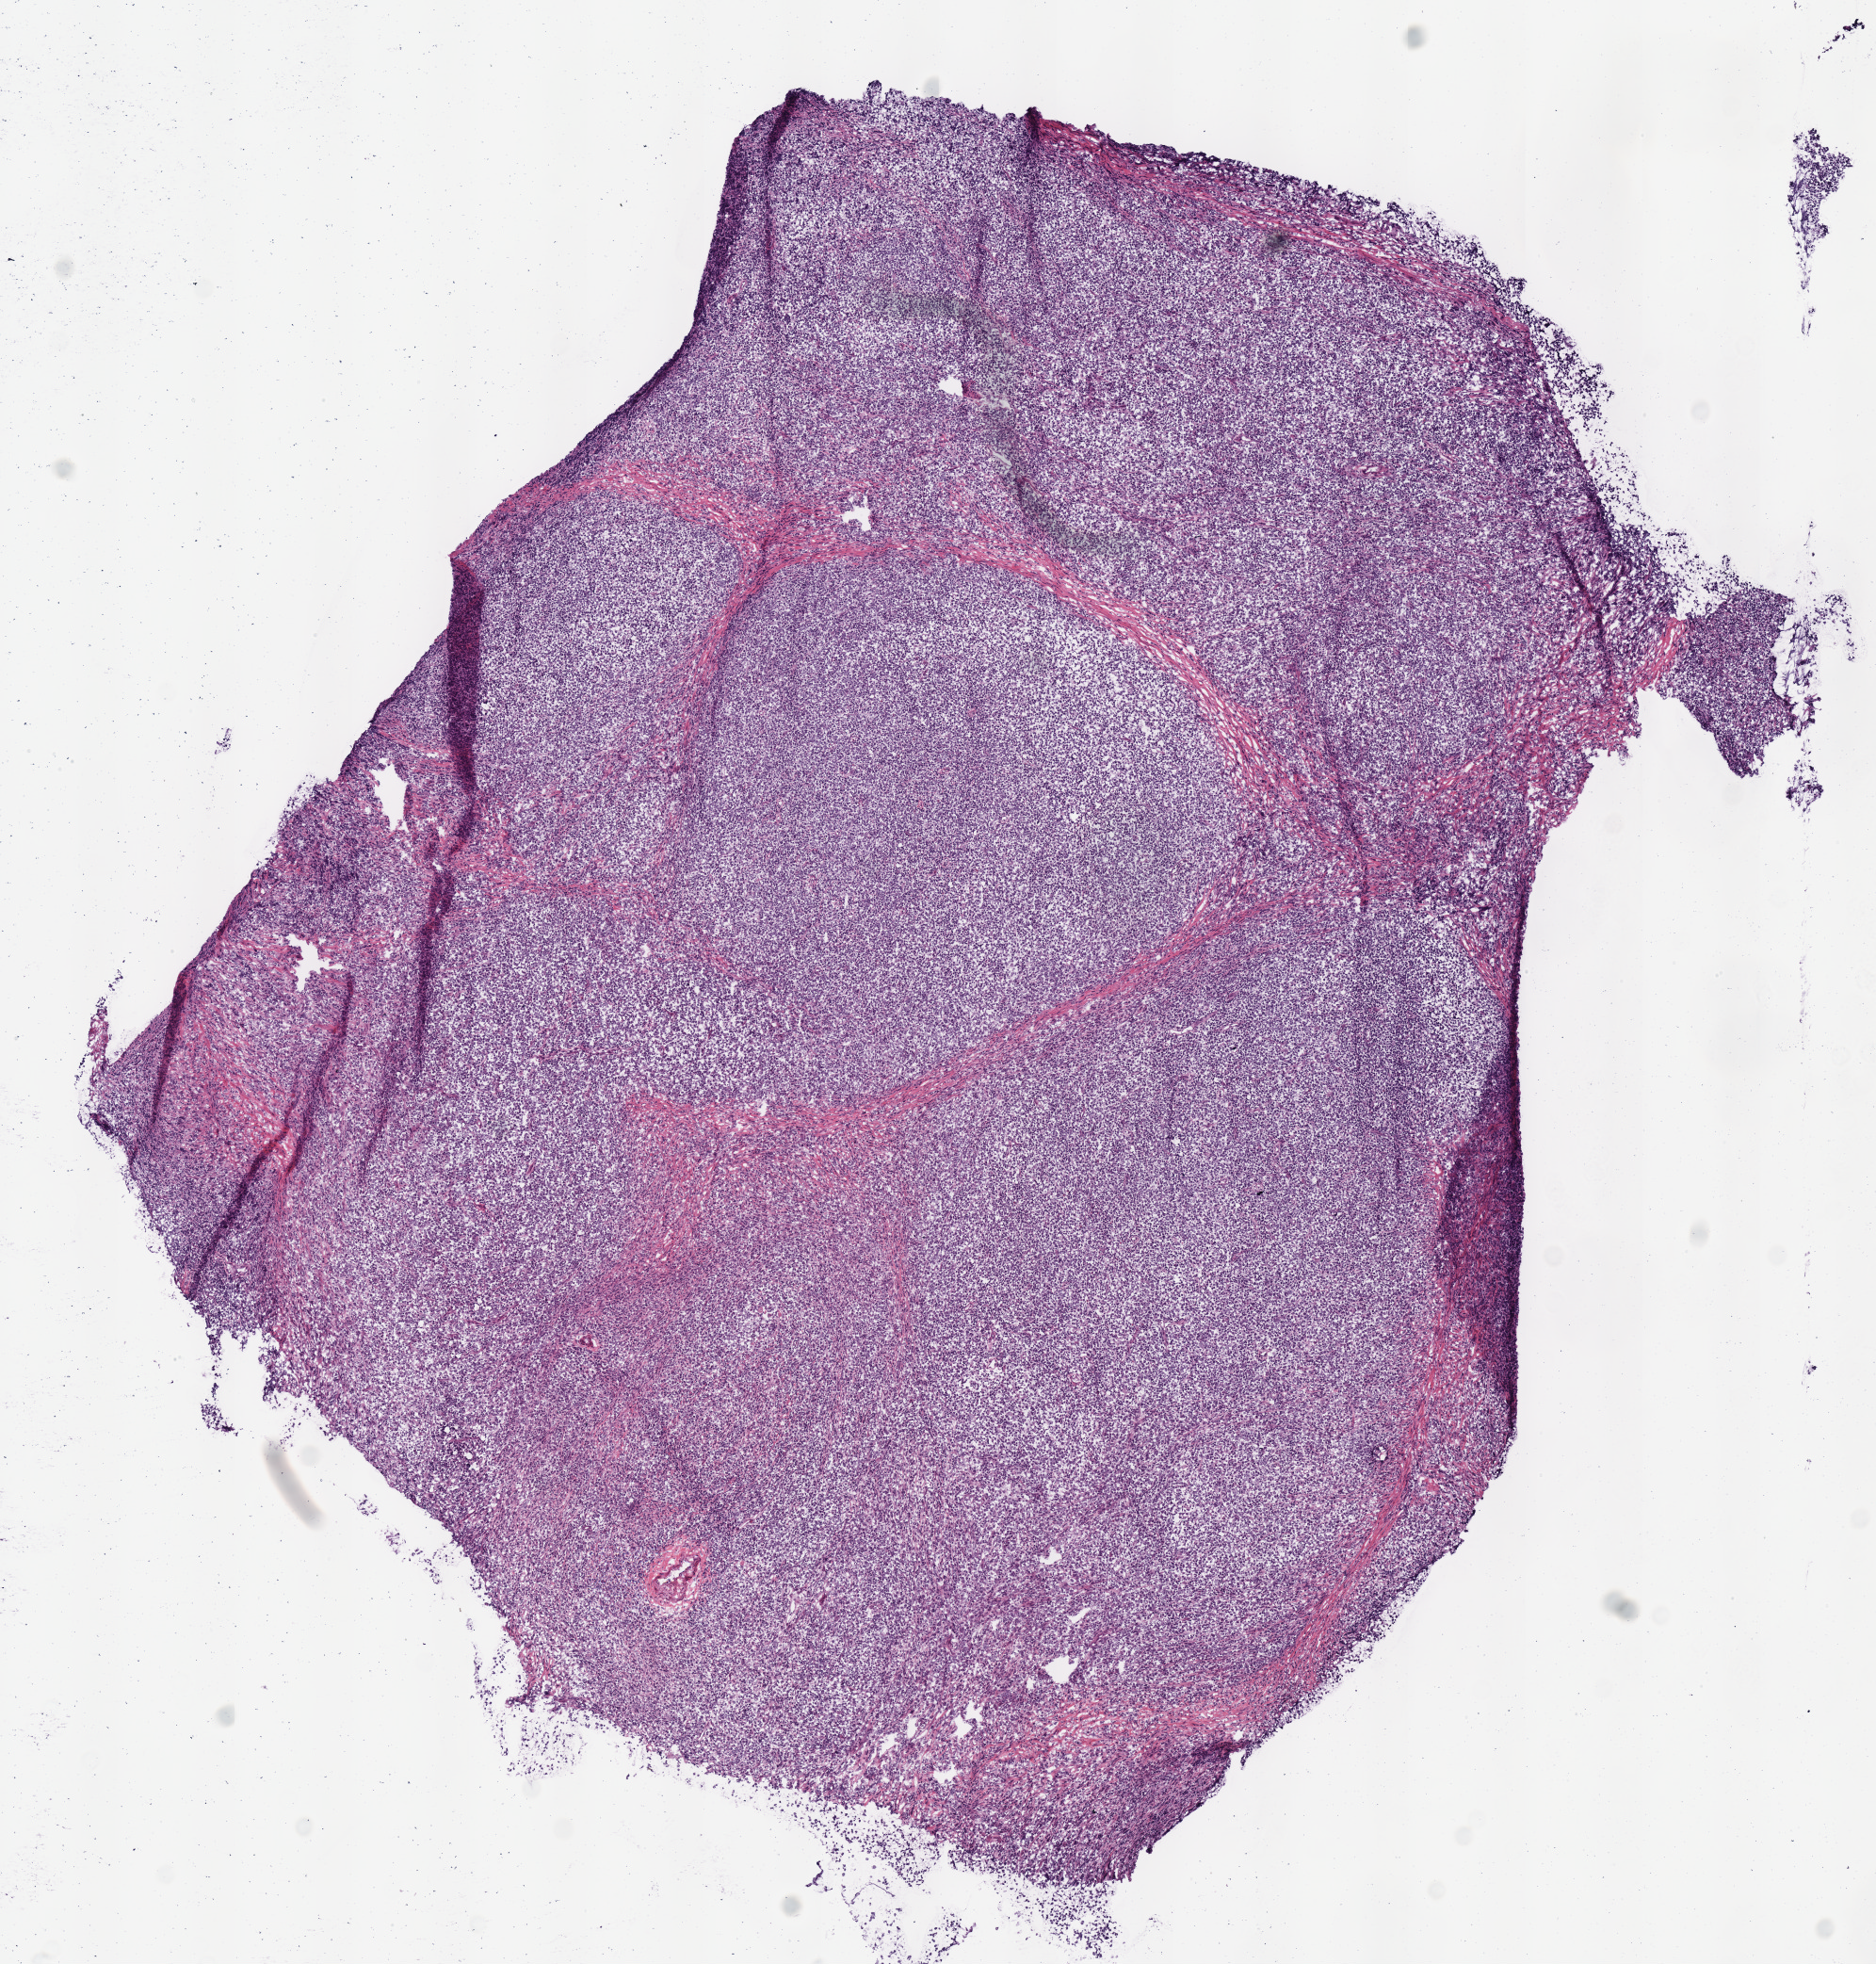
H&E whole-slide image, low-resolution overview of the scanned area, about 7.8 x 8.2 mm. Frozen section from the bottom of the tissue portion. Sample: primary tumour, lymphoid tissue. Patient: male, age at initial diagnosis 42 years. Pathologist review of this section (percent, as recorded): tumour cells 90%, tumour nuclei 95%, normal cells 0%, stromal cells 10%, necrosis 0%.
Pathologic diagnosis: Diffuse large B-cell lymphoma, NOS (small intestine, NOS).